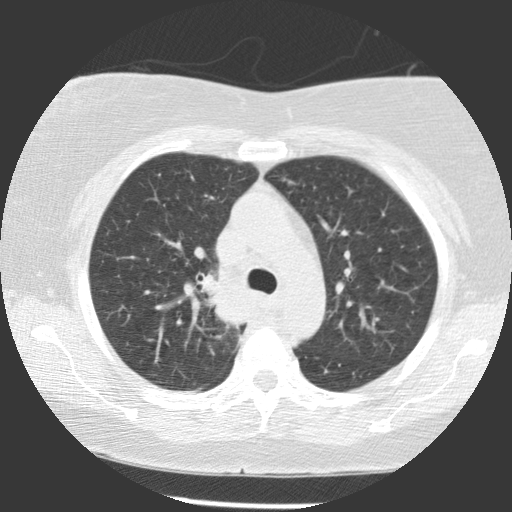
Low-dose screening chest CT, axial slice; baseline annual screen; lung window (W 1500 / L -600 HU); 140 kVp; slice 82 of 116 in the series; 512 × 512 image matrix, field of view 320 × 320 mm. Female participant, aged 63 years at enrolment. Former smoker at enrolment.
- Expert reader's lesion annotation, bounding box (x1, y1, x2, y2) in pixels: (189, 263, 251, 324).
- The exam's reader record, not a measurement of the box and not confirmed to be the same lesion: non-calcified nodule or mass ≥4 mm, right upper lobe, 39 × 36 mm, spiculated (stellate) margins, soft tissue attenuation.
- Official screen result: positive, change unspecified: nodule(s) >= 4 mm or enlarging nodule(s), mass(es), or other non-specific abnormalities suspicious for lung cancer.
- Later outcome: lung cancer diagnosed 72 days after this screen — non-small cell carcinoma, right upper lobe, carina, right main stem bronchus, poorly differentiated (G3), stage IIIA (AJCC 6th edition), 66 mm at pathology.